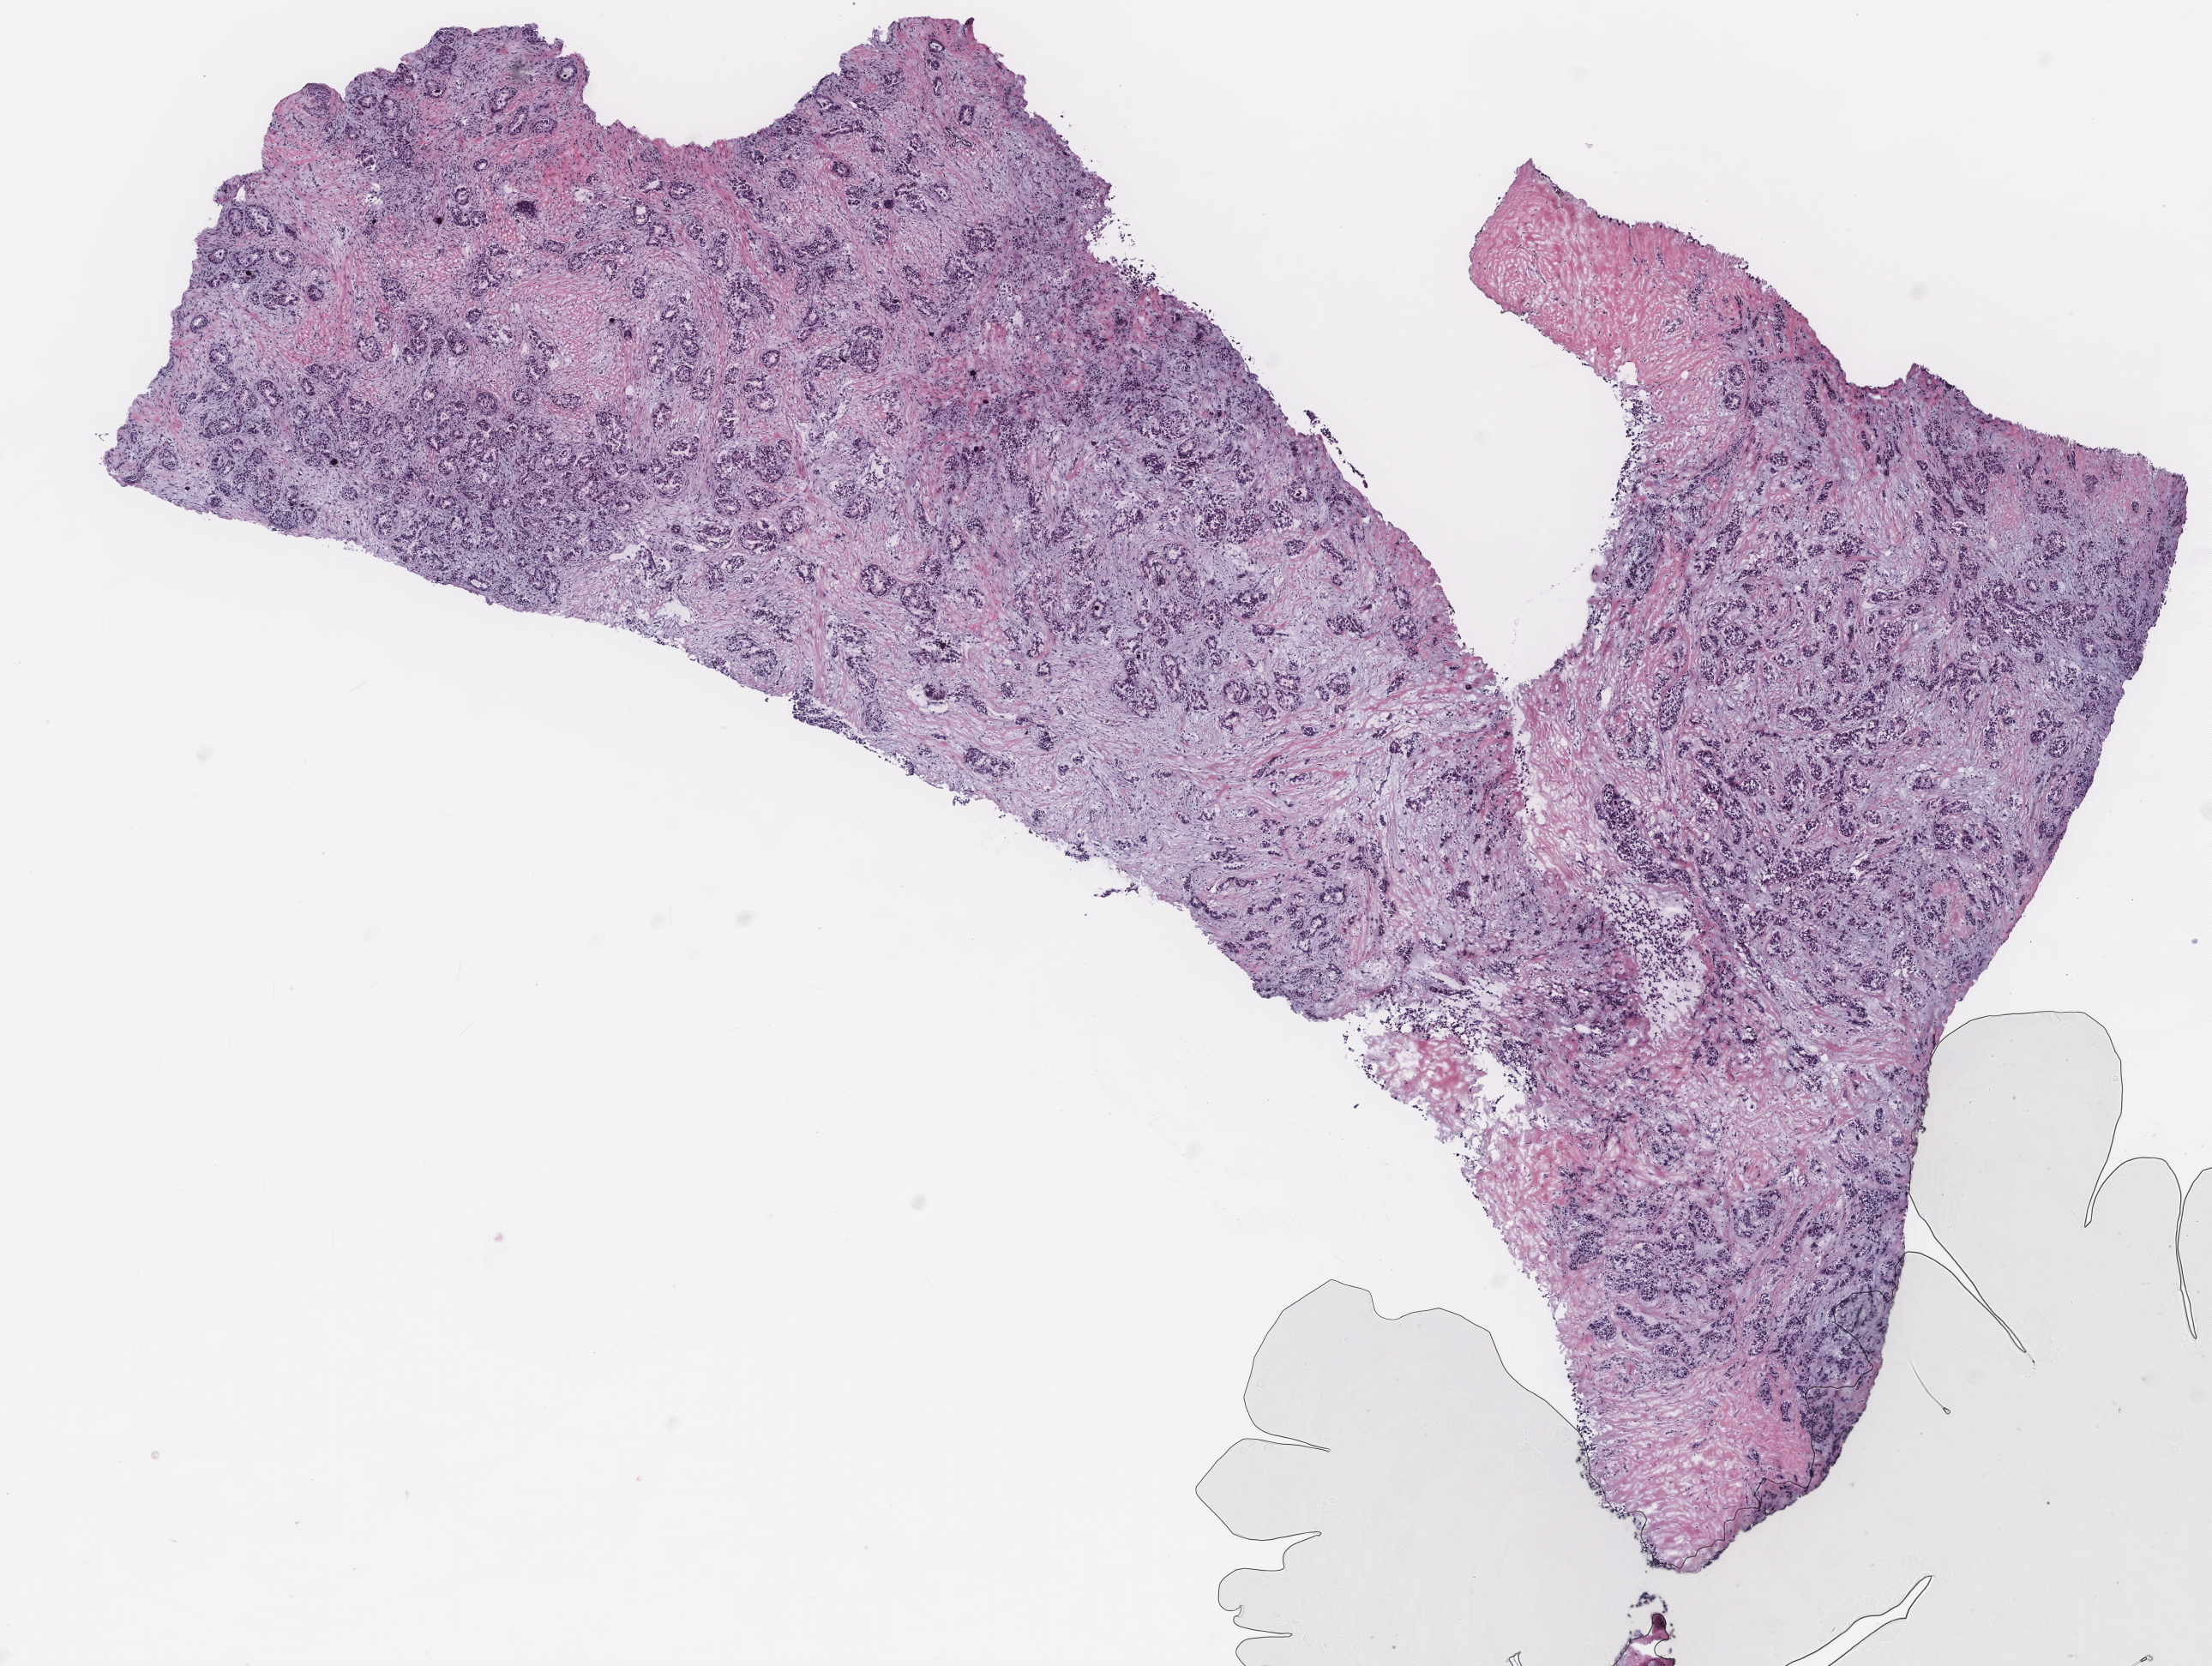
Digitized Hematoxylin and eosin (H&E) stained tissue section (whole slide) — whole scanned area (about 10.3 x 7.8 mm) shown as a low-resolution overview; breast, tissue type not recorded. 60-year-old female patient.
• patient diagnosis: Infiltrating duct carcinoma, NOS